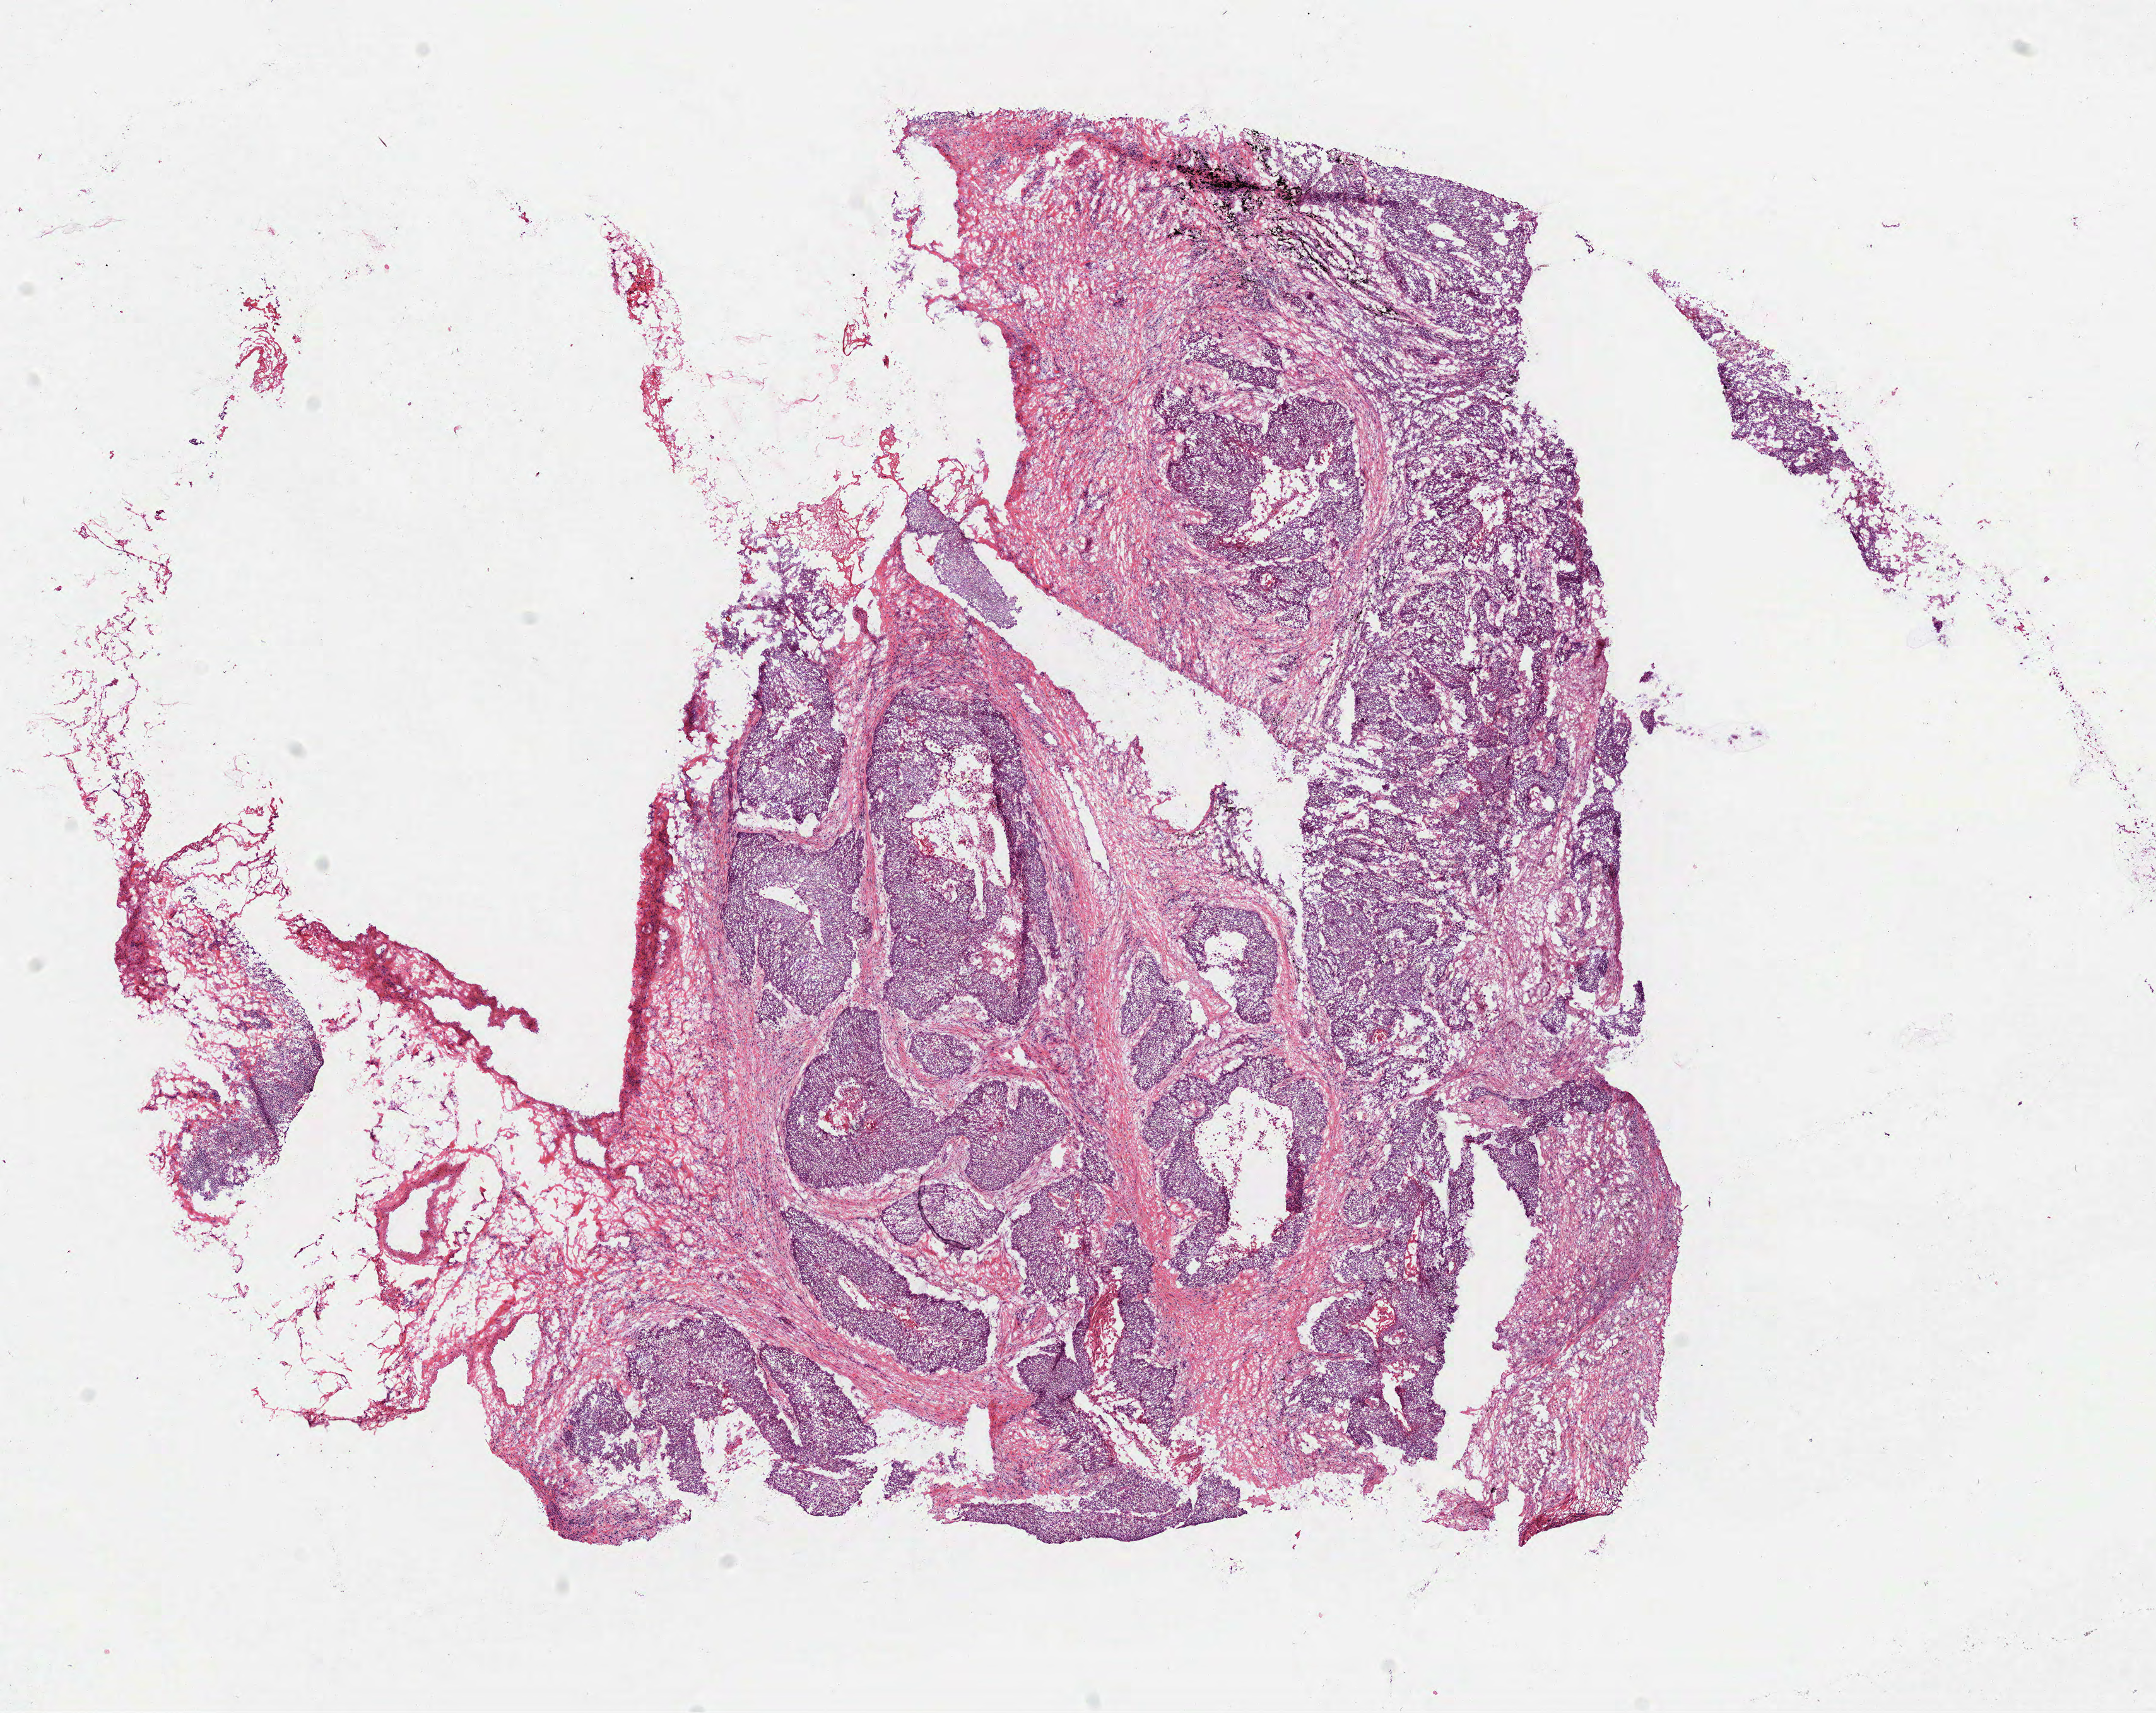
Digitized H&E-stained tissue section (whole slide), a low-resolution overview of the entire scanned area, about 13.8 x 10.9 mm (slide scanned at 40x); frozen section from the bottom of the tissue portion; primary tumour sample from the lung. Patient: male, age at initial diagnosis 70 years. Slide review estimates, as recorded: tumour cells 70%, tumour nuclei 70%, normal cells 0%, stromal cells 26%, necrosis 4%. Infiltration values recorded for this section: lymphocyte infiltration 18%, monocyte infiltration 0%, neutrophil infiltration 2%.
• histologic diagnosis: Squamous cell carcinoma, NOS (lower lobe, lung)
• AJCC pathologic stage: II (7th edition)
• laterality: right